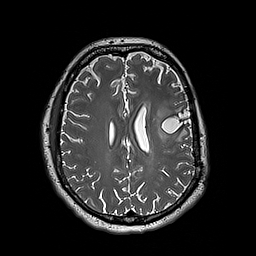
Brain MRI from a brain-tumour surgery series, one axial slice. Slice 80 of 192 in the series (ordered by position). 1 mm slice thickness. 256 × 256 image matrix, field of view 250 × 250 mm. Case-level facts recorded for this patient, not image findings: histopathology: Astrocytoma; WHO grade: 3.
Annotated regions visible in this slice (expert manual segmentation):
- tumour: bounding box [x1, y1, x2, y2] px = [152, 98, 175, 142]